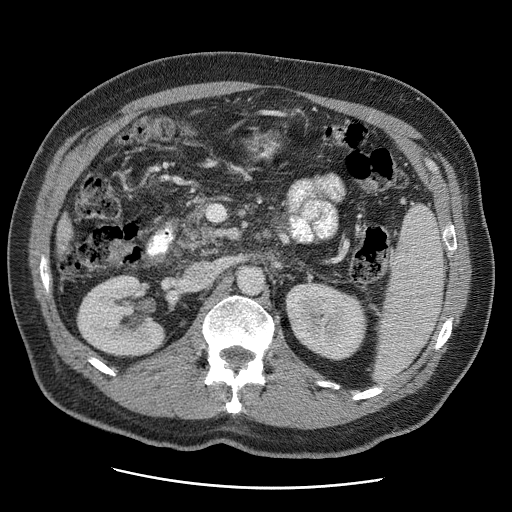
Contrast-enhanced abdominal CT (liver protocol), one axial slice. Slice 7 of 81 in the series (ordered by position). Reconstruction kernel STANDARD. Soft-tissue window (W 400 / L 40 HU). 2.5 mm slice thickness. 512 × 512 image matrix, field of view 380 × 380 mm. From the clinical record (not read from this slice): diagnosis: hepatocellular carcinoma (patient treated with transarterial chemoembolisation; whether this scan precedes or follows treatment is not stated here); TNM stage (as recorded): Stage-IIIA; Child-Pugh class: A; tumour differentiation: moderately differentiated; tumour nodularity: multinodular.
Structures marked on this image (semi-automatic segmentation, software-assisted and operator-edited):
- liver parenchyma outside the tumour (the mass and vessels are separate outlines, so this box may not span the whole liver): bounding box (x1, y1, x2, y2) in pixels: (56, 213, 72, 254)